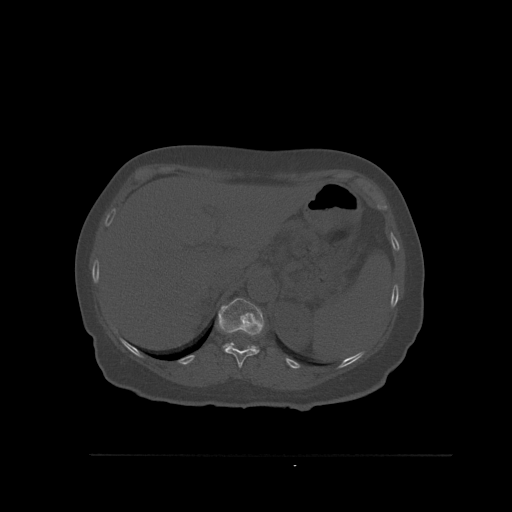
CT including the spine, one axial slice; slice 297 of 527 in the series (ordered by position); bone window (W 1800 / L 400 HU); 1.5 mm slice thickness; 512 × 512 image matrix, field of view 470 × 470 mm. Patient: female, 73 years. From the clinical record (not read from this slice): primary cancer: breast.
Outlined on this slice (semi-automatic segmentation, software-assisted and operator-edited):
- T11 vertebra: bounding box (x1, y1, x2, y2) in pixels: (223, 347, 259, 368)
- T12 vertebra: (216, 298, 265, 350)